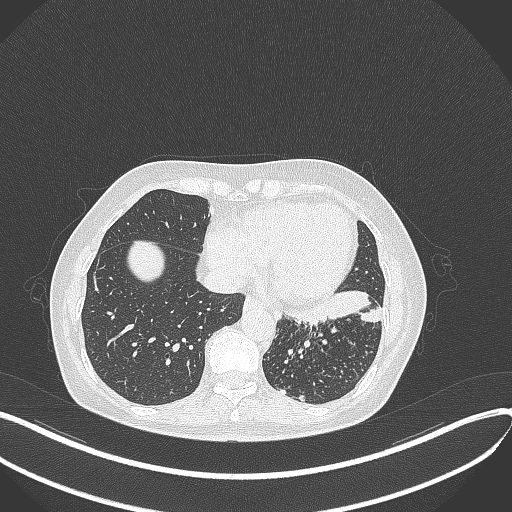
Chest CT, one axial slice. Position 125 of 429 along the scan axis. Reconstruction kernel B70f. 100 kVp. Lung window (W 1500 / L -600 HU). 1 mm slice thickness. 512 × 512 image matrix, field of view 400 × 400 mm. Female patient, age 63 years. From the clinical record (not read from this slice): clinical TNM (as recorded): T1b N0 M0.
Structures marked on this image (rectangle marked by the reading radiologist):
- lung tumour (recorded histology: adenocarcinoma): bounding box <284,290,385,326> (left, top, right, bottom; pixels)